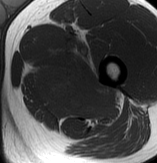
MRI of an extremity soft-tissue mass, one axial slice; position 60 of 70 along the scan axis; MR volume resampled by the dataset authors to the PET/CT grid (not the native acquisition matrix); 3.27 mm slice thickness; 157 × 163 image matrix, field of view 153 × 159 mm. Male patient. Case-level facts recorded for this patient, not image findings: histological type: extraskeletal osteosarcoma; grade: high; site of the primary tumour: left adductur.
Annotated regions visible in this slice (expert contour drawn on MRI and transferred to this co-registered scan by the dataset authors):
- gross tumour volume (mass): bounding box [x1, y1, x2, y2] px = [33, 35, 121, 125]